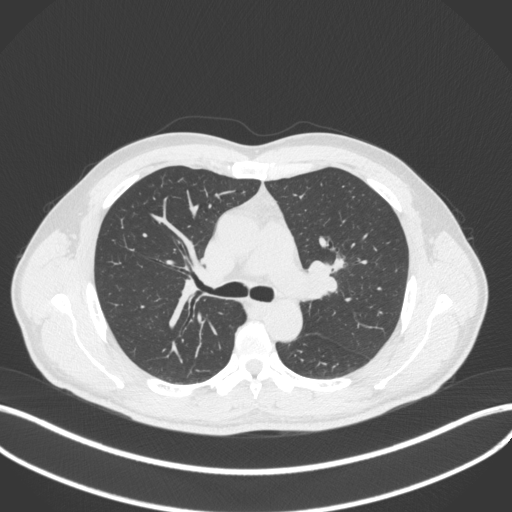
Chest CT, one axial slice; slice 273 of 383 in the series (ordered by position); lung window (W 1500 / L -600 HU); 1 mm slice thickness; 512 × 512 image matrix. Patient: male, 50 years. From the clinical record (not read from this slice): clinical TNM (as recorded): T1c N1 M1b.
Annotated regions visible in this slice (bounding box drawn by a radiologist):
- lung tumour (recorded histology: squamous cell carcinoma): box from (x=332, y=254) to (x=347, y=277) px